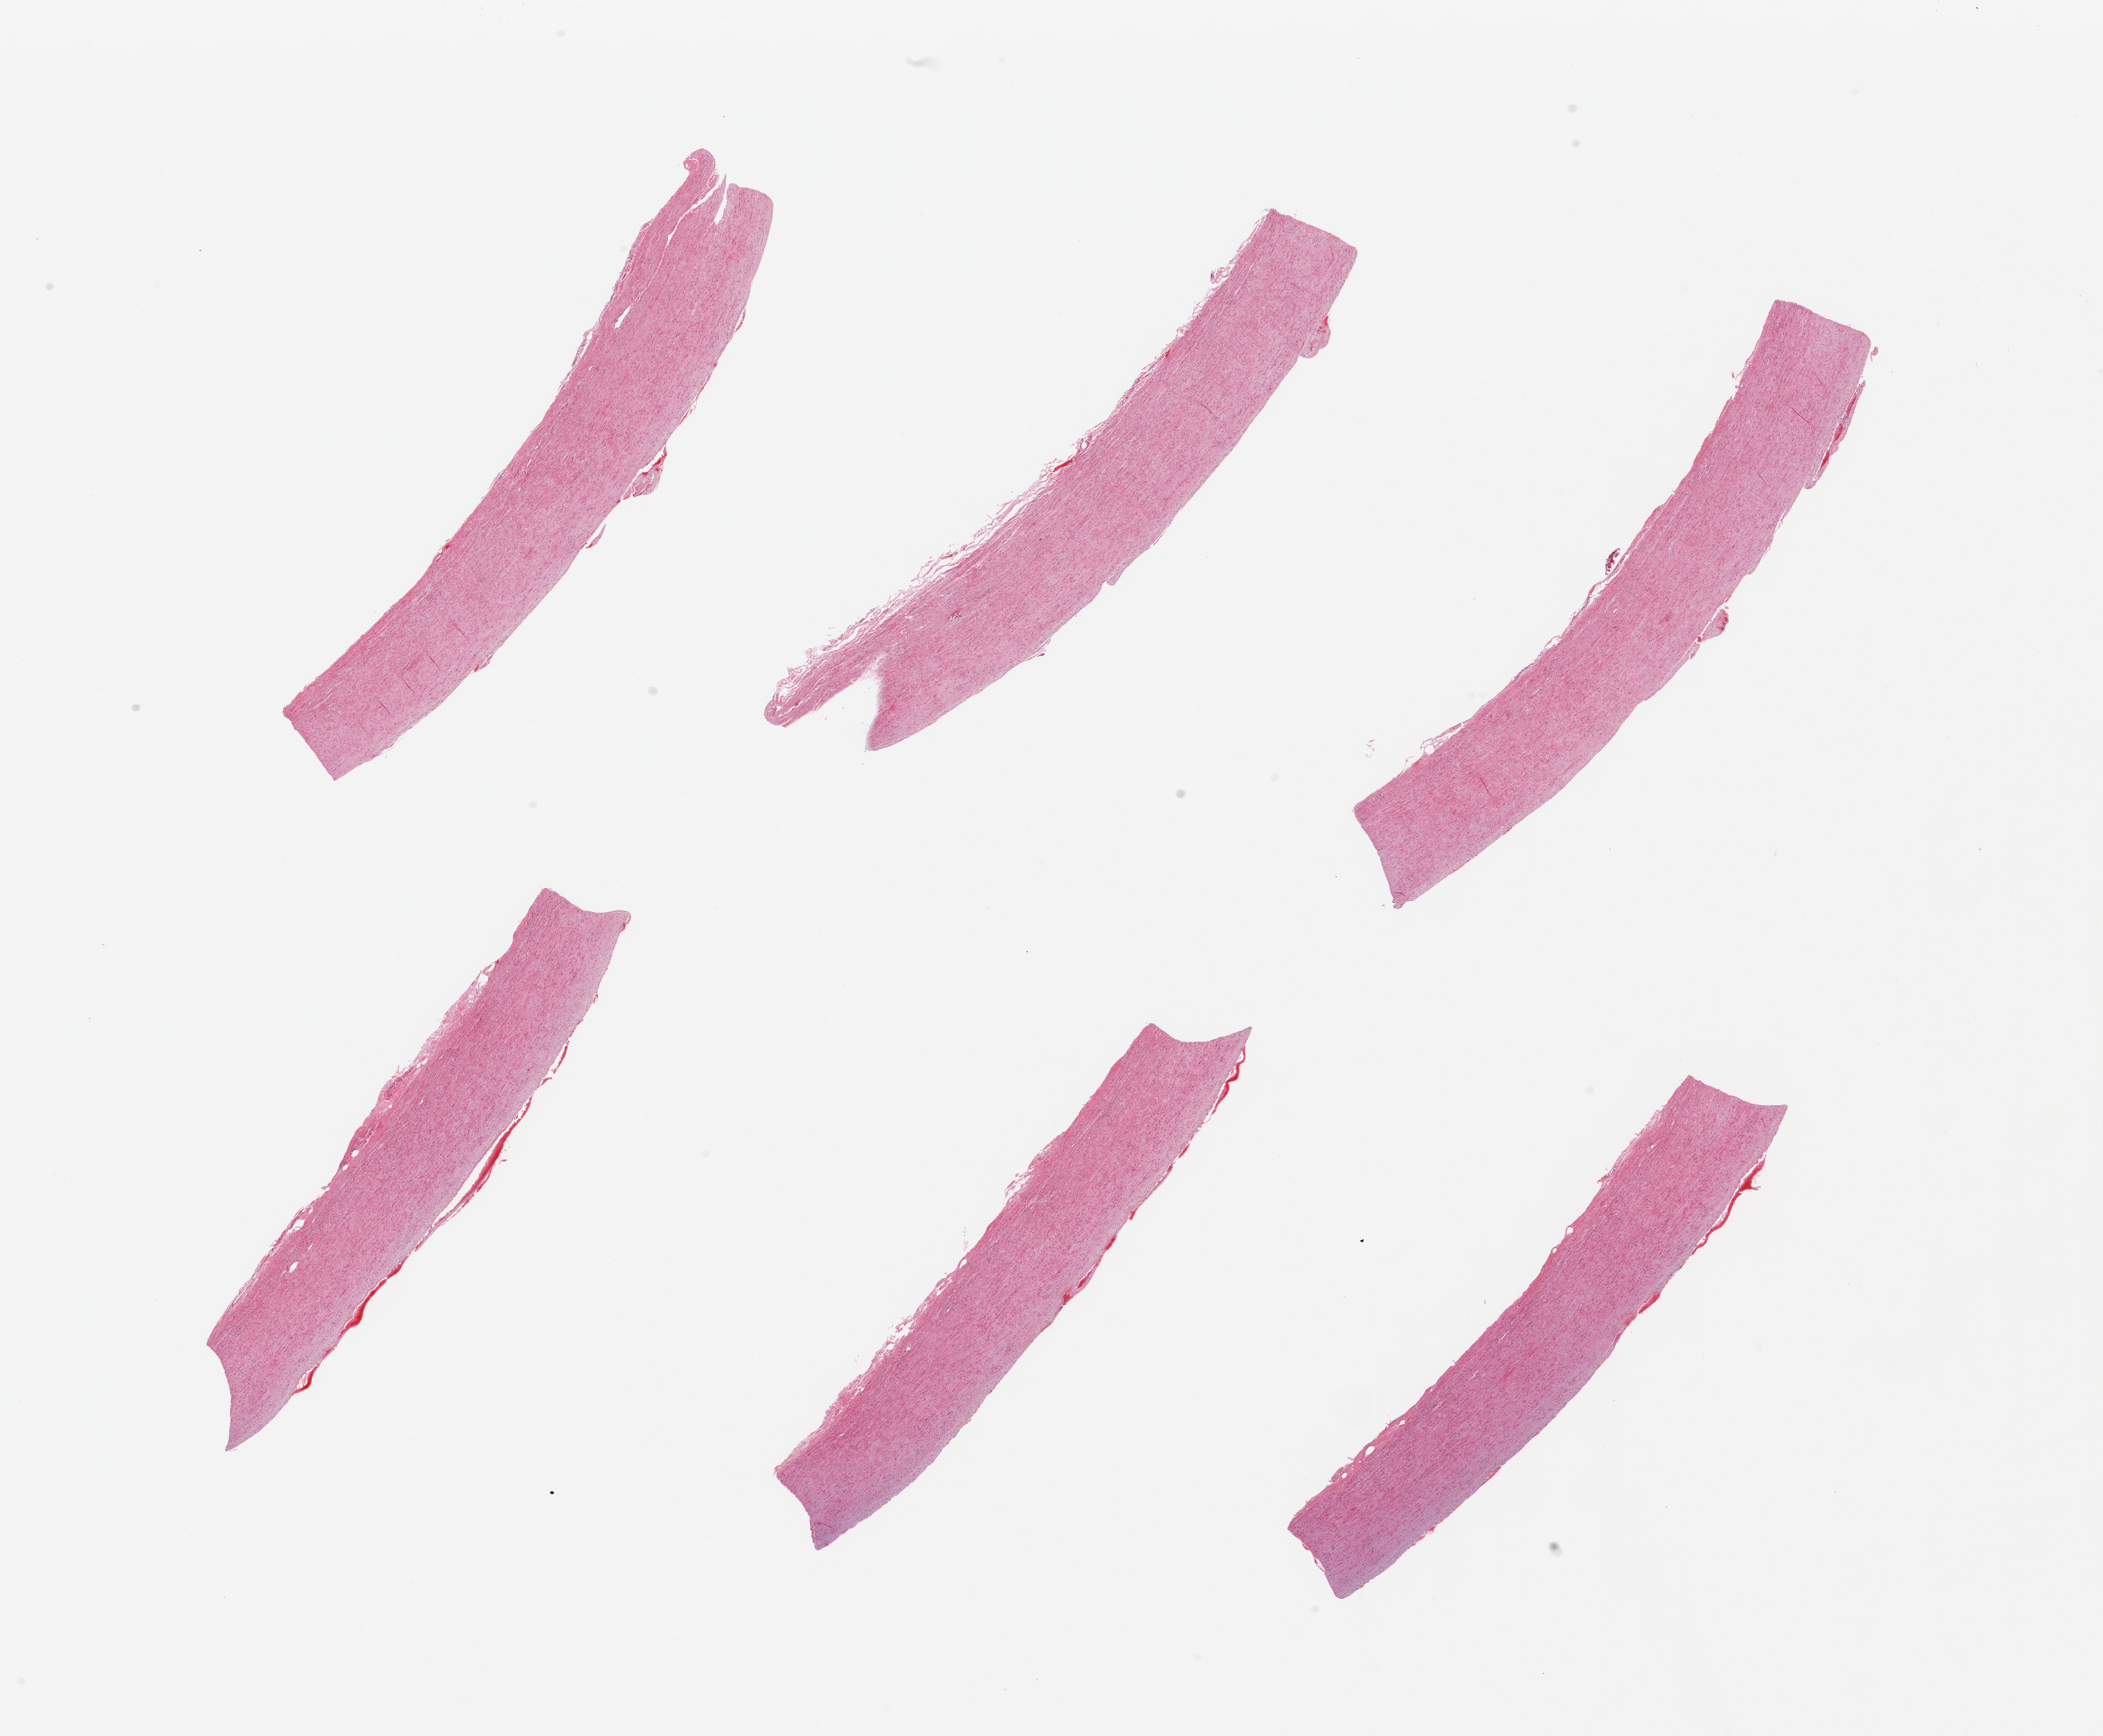
Whole-slide image, H&E stain — whole scanned area (about 25.6 x 21.1 mm) shown as a low-resolution overview; PAXgene-fixed, paraffin-embedded tissue; section of aorta (target tissue); donor tissue sample. Male donor.
Pathologist's review note for this sample: 6 pieces; well trimmed; flat plaques.